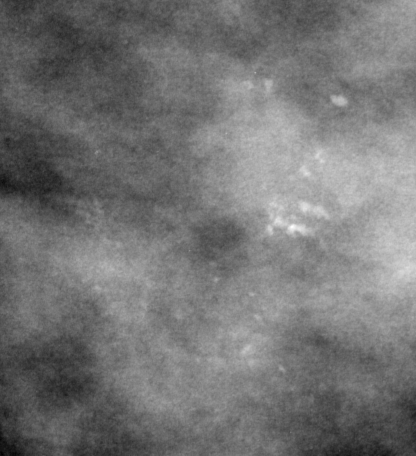
Cropped region of a digitized screen-film mammogram centred on a radiologist-marked abnormality, left breast, CC view, BI-RADS breast density category 4 (scale 1–4).
- Calcifications, morphology pleomorphic, distribution clustered; BI-RADS assessment category 4; pathology result (as recorded, not read from the image): malignant.